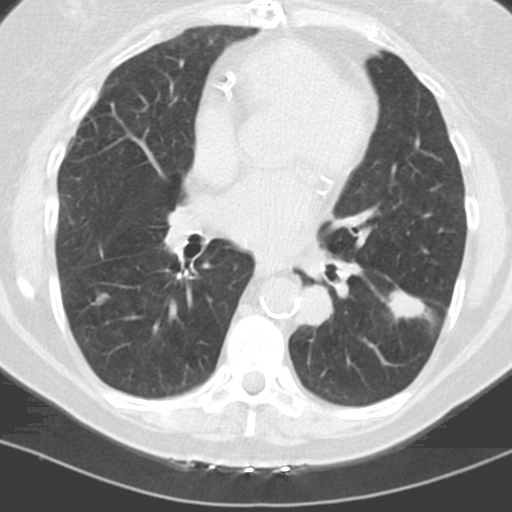
Axial slice from a low-dose chest CT screening exam; first (baseline) screen; lung window (W 1500 / L -600 HU); 120 kVp; 512 × 512 image matrix, field of view 278 × 278 mm. Female, age 60 years at enrolment.
2 lesions marked by an expert reader on this slice (largest first), bounding box (x1, y1, x2, y2) in pixels: (290, 281, 339, 333); (374, 286, 427, 331). The screening reader recorded 3 non-calcified nodules or masses ≥4 mm on this exam; which of them these boxes mark is not recorded. Lung cancer was diagnosed 96 days after this screen: adenocarcinoma, NOS, left lower lobe, stage IV (AJCC 6th edition), 22 mm at pathology.